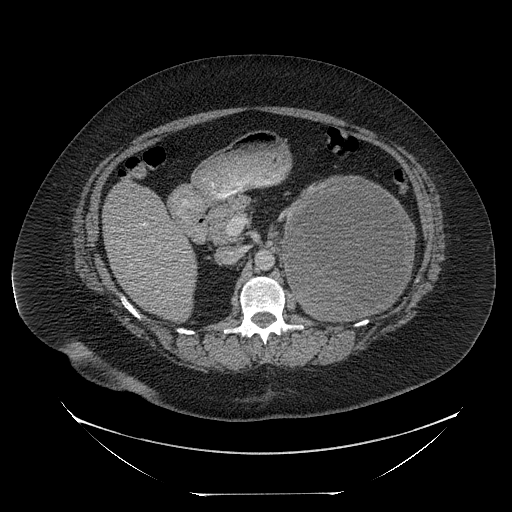
Contrast-enhanced abdominal CT, one axial slice. Slice 135 of 205 in the series (ordered by position). Reconstruction kernel STANDARD. 120 kVp. Intravenous contrast given. Soft-tissue window (W 400 / L 40 HU). 512 × 512 image matrix, field of view 500 × 500 mm. Female patient, age 53 years. From the clinical record (not read from this slice): diagnosis: adrenocortical carcinoma; tumour side: left adrenal.
Structures marked on this image (semi-automatic segmentation, software-assisted and operator-edited):
- mass: bounding box (x1, y1, x2, y2) in pixels: (284, 179, 412, 320)